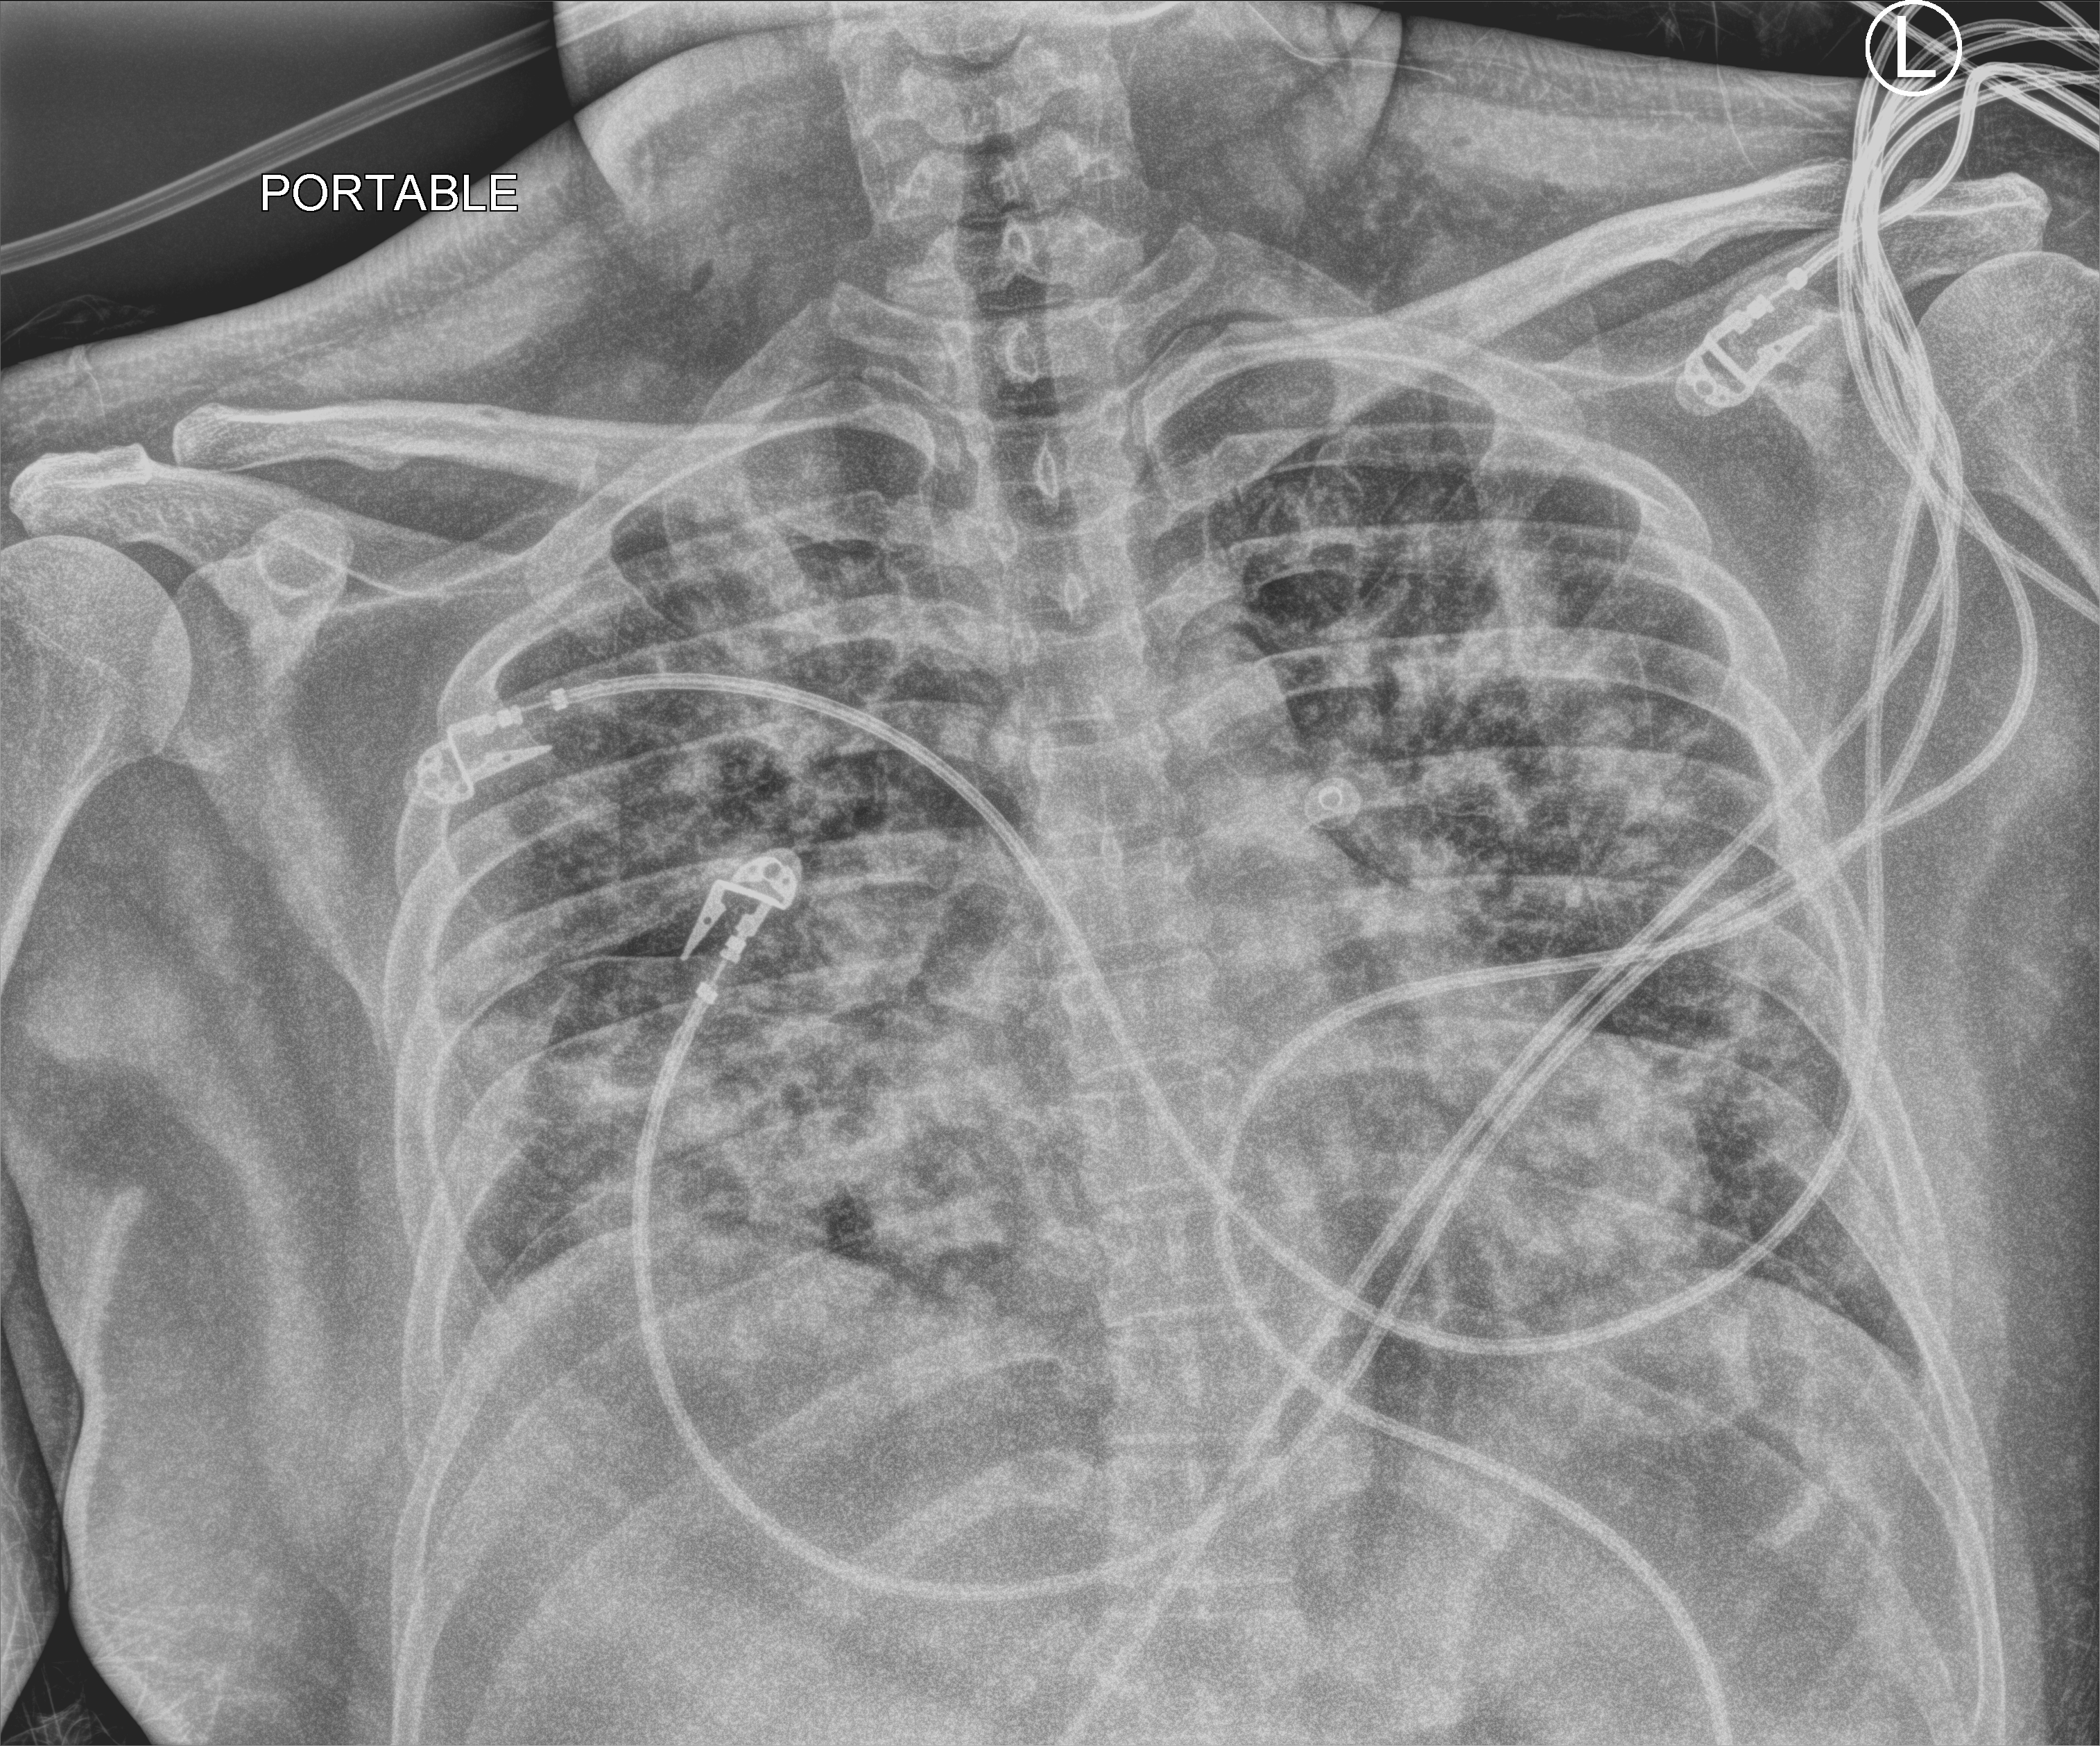
Chest X-ray (portable), anteroposterior (AP) projection. Male patient hospitalised with COVID-19, age 18–59 years.
Hospital-stay facts (about this admission, not read from this image; timing relative to this image not recorded): smoking status (admission record): never; mechanically ventilated during this hospital stay: no; other chronic lung disease (admission record): yes.